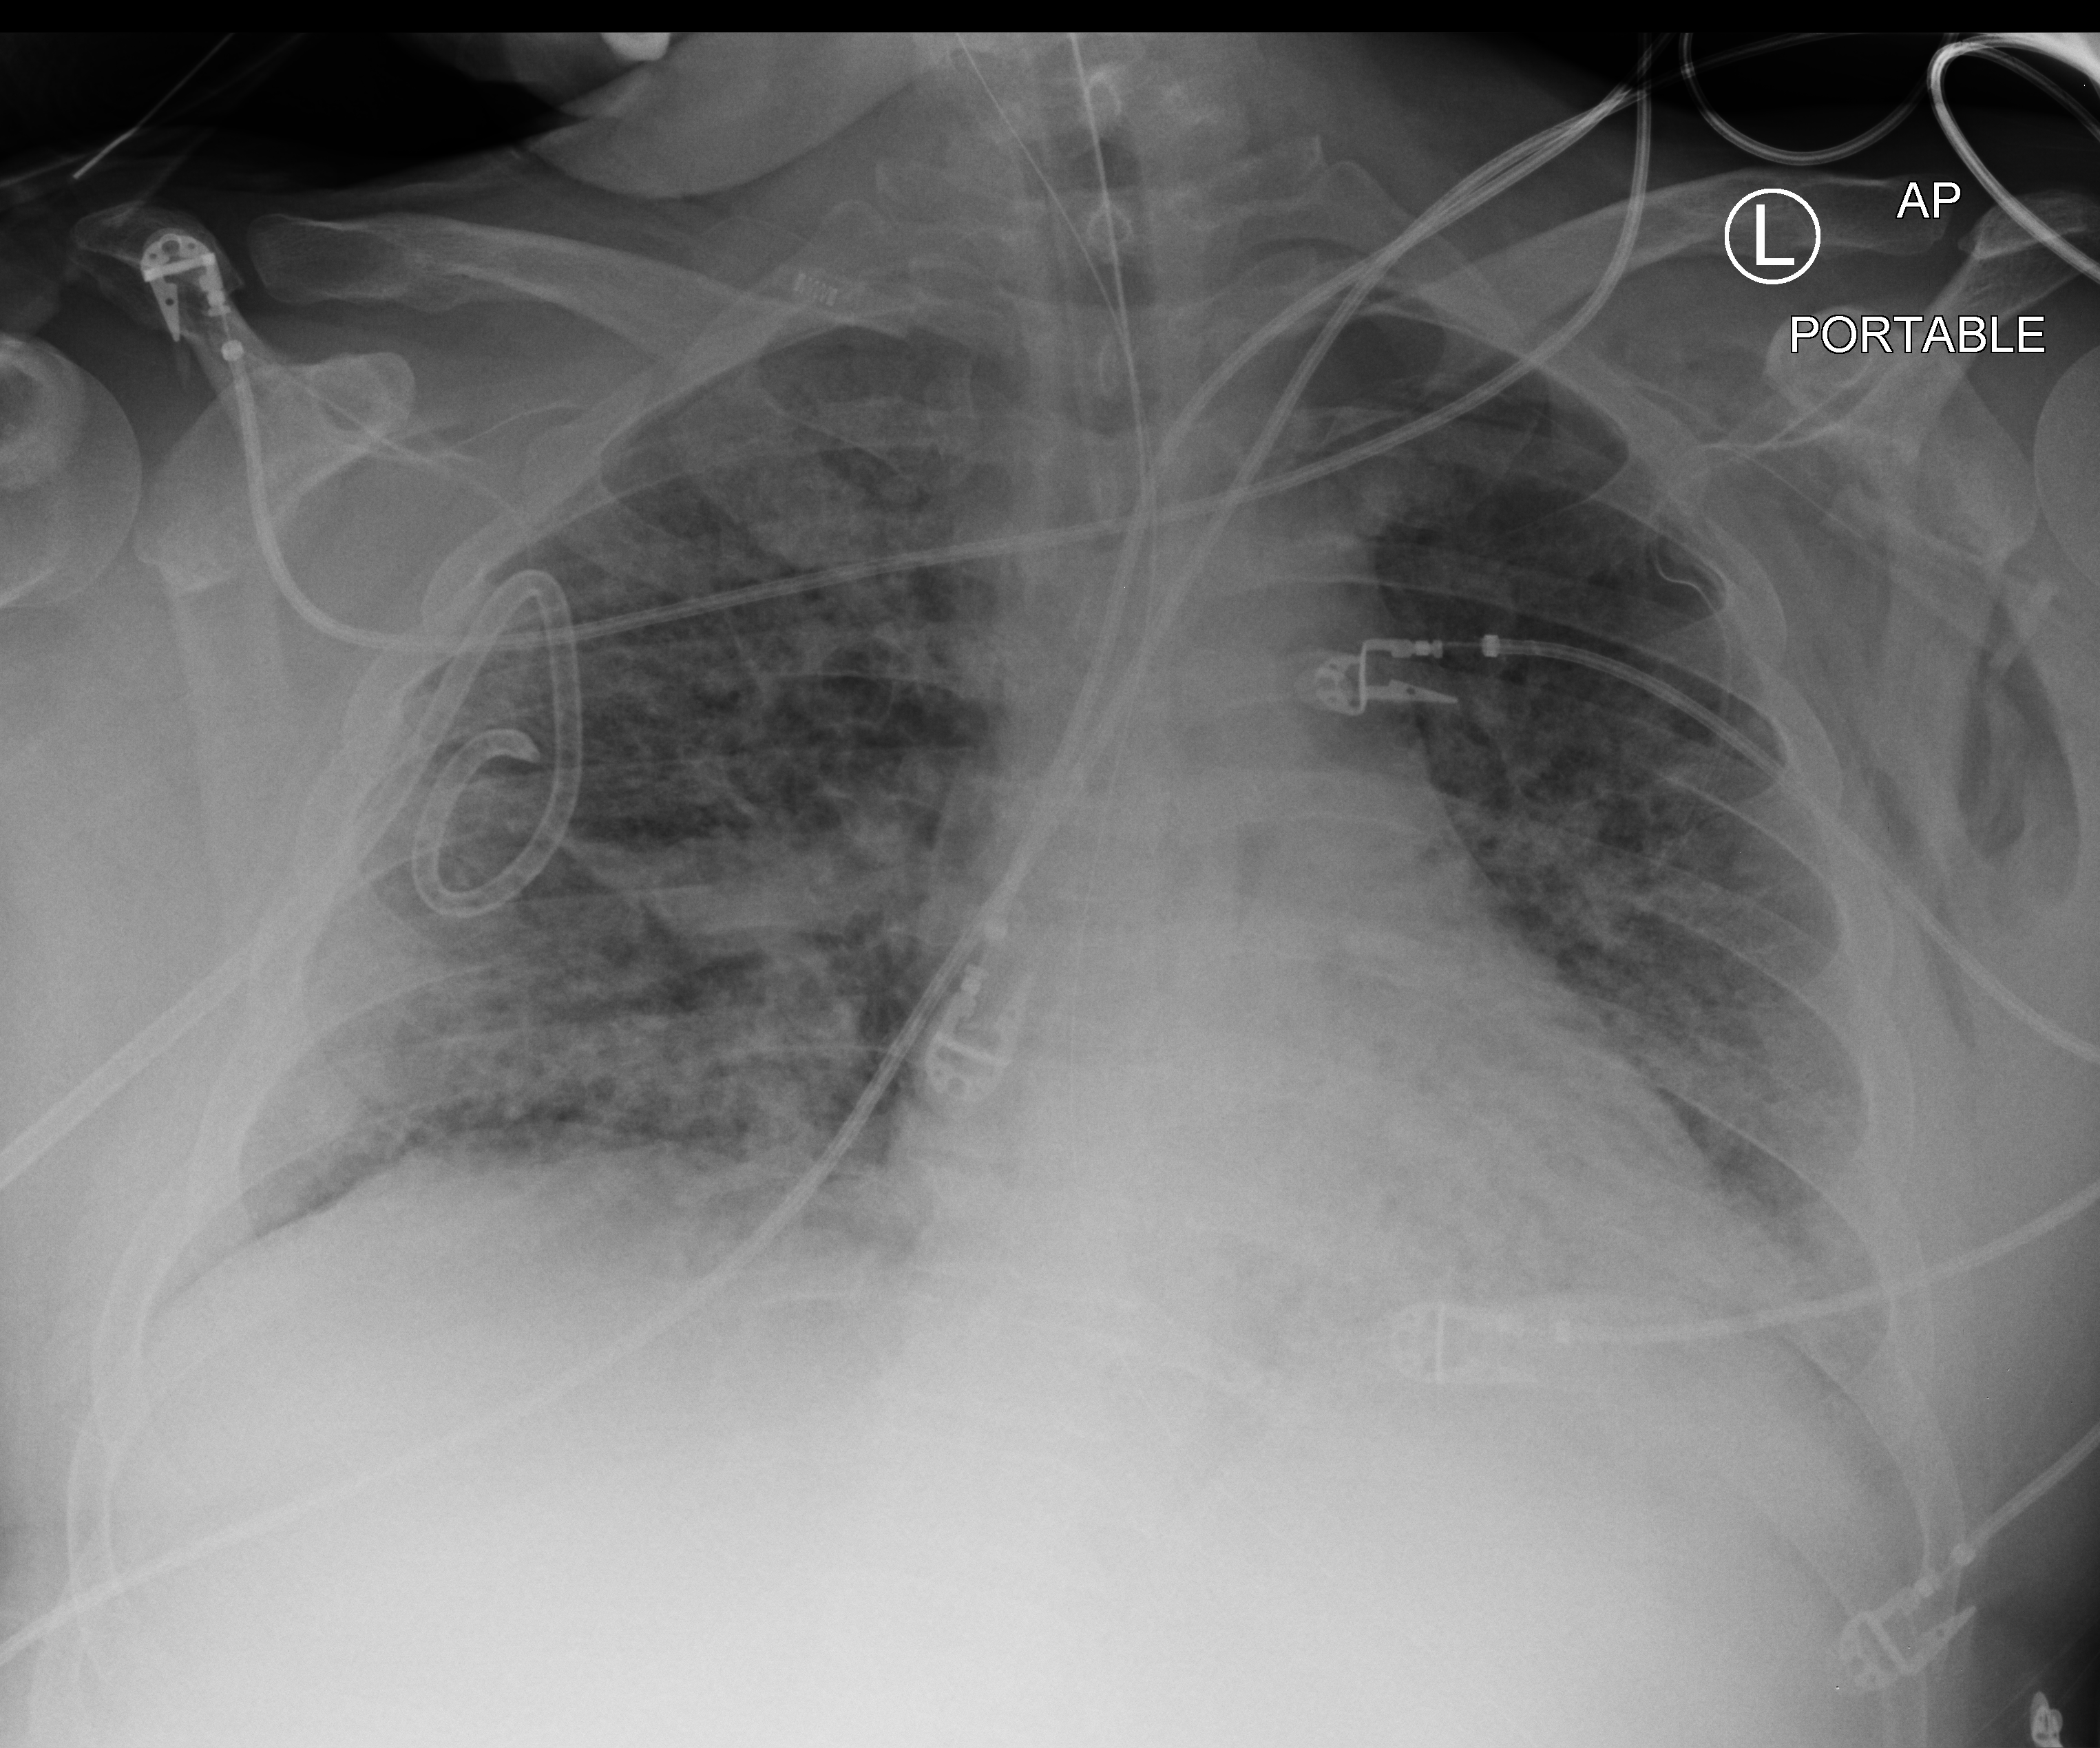
Portable chest radiograph; anteroposterior (AP) projection. Adult patient hospitalised with COVID-19, age 18–59 years.
Admission-level facts for this patient (not findings on this image; timing relative to this image not recorded): mechanically ventilated during this hospital stay: yes.